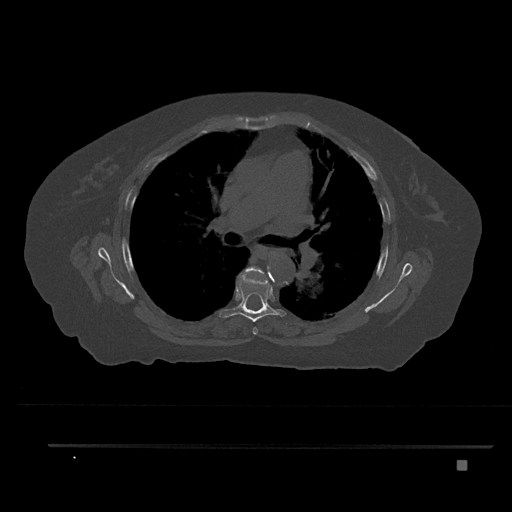
CT including the spine, one axial slice. Position 534 of 797 along the scan axis. Bone window (W 1800 / L 400 HU). 0.5 mm slice thickness. 512 × 512 image matrix, field of view 437 × 437 mm. Female patient, age 76 years. From the clinical record (not read from this slice): primary cancer: lung.
Annotated regions visible in this slice (semi-automatically segmented with operator editing):
- T5 vertebra: bounding box <245,266,268,335> (left, top, right, bottom; pixels)
- T6 vertebra: <219,272,286,322>